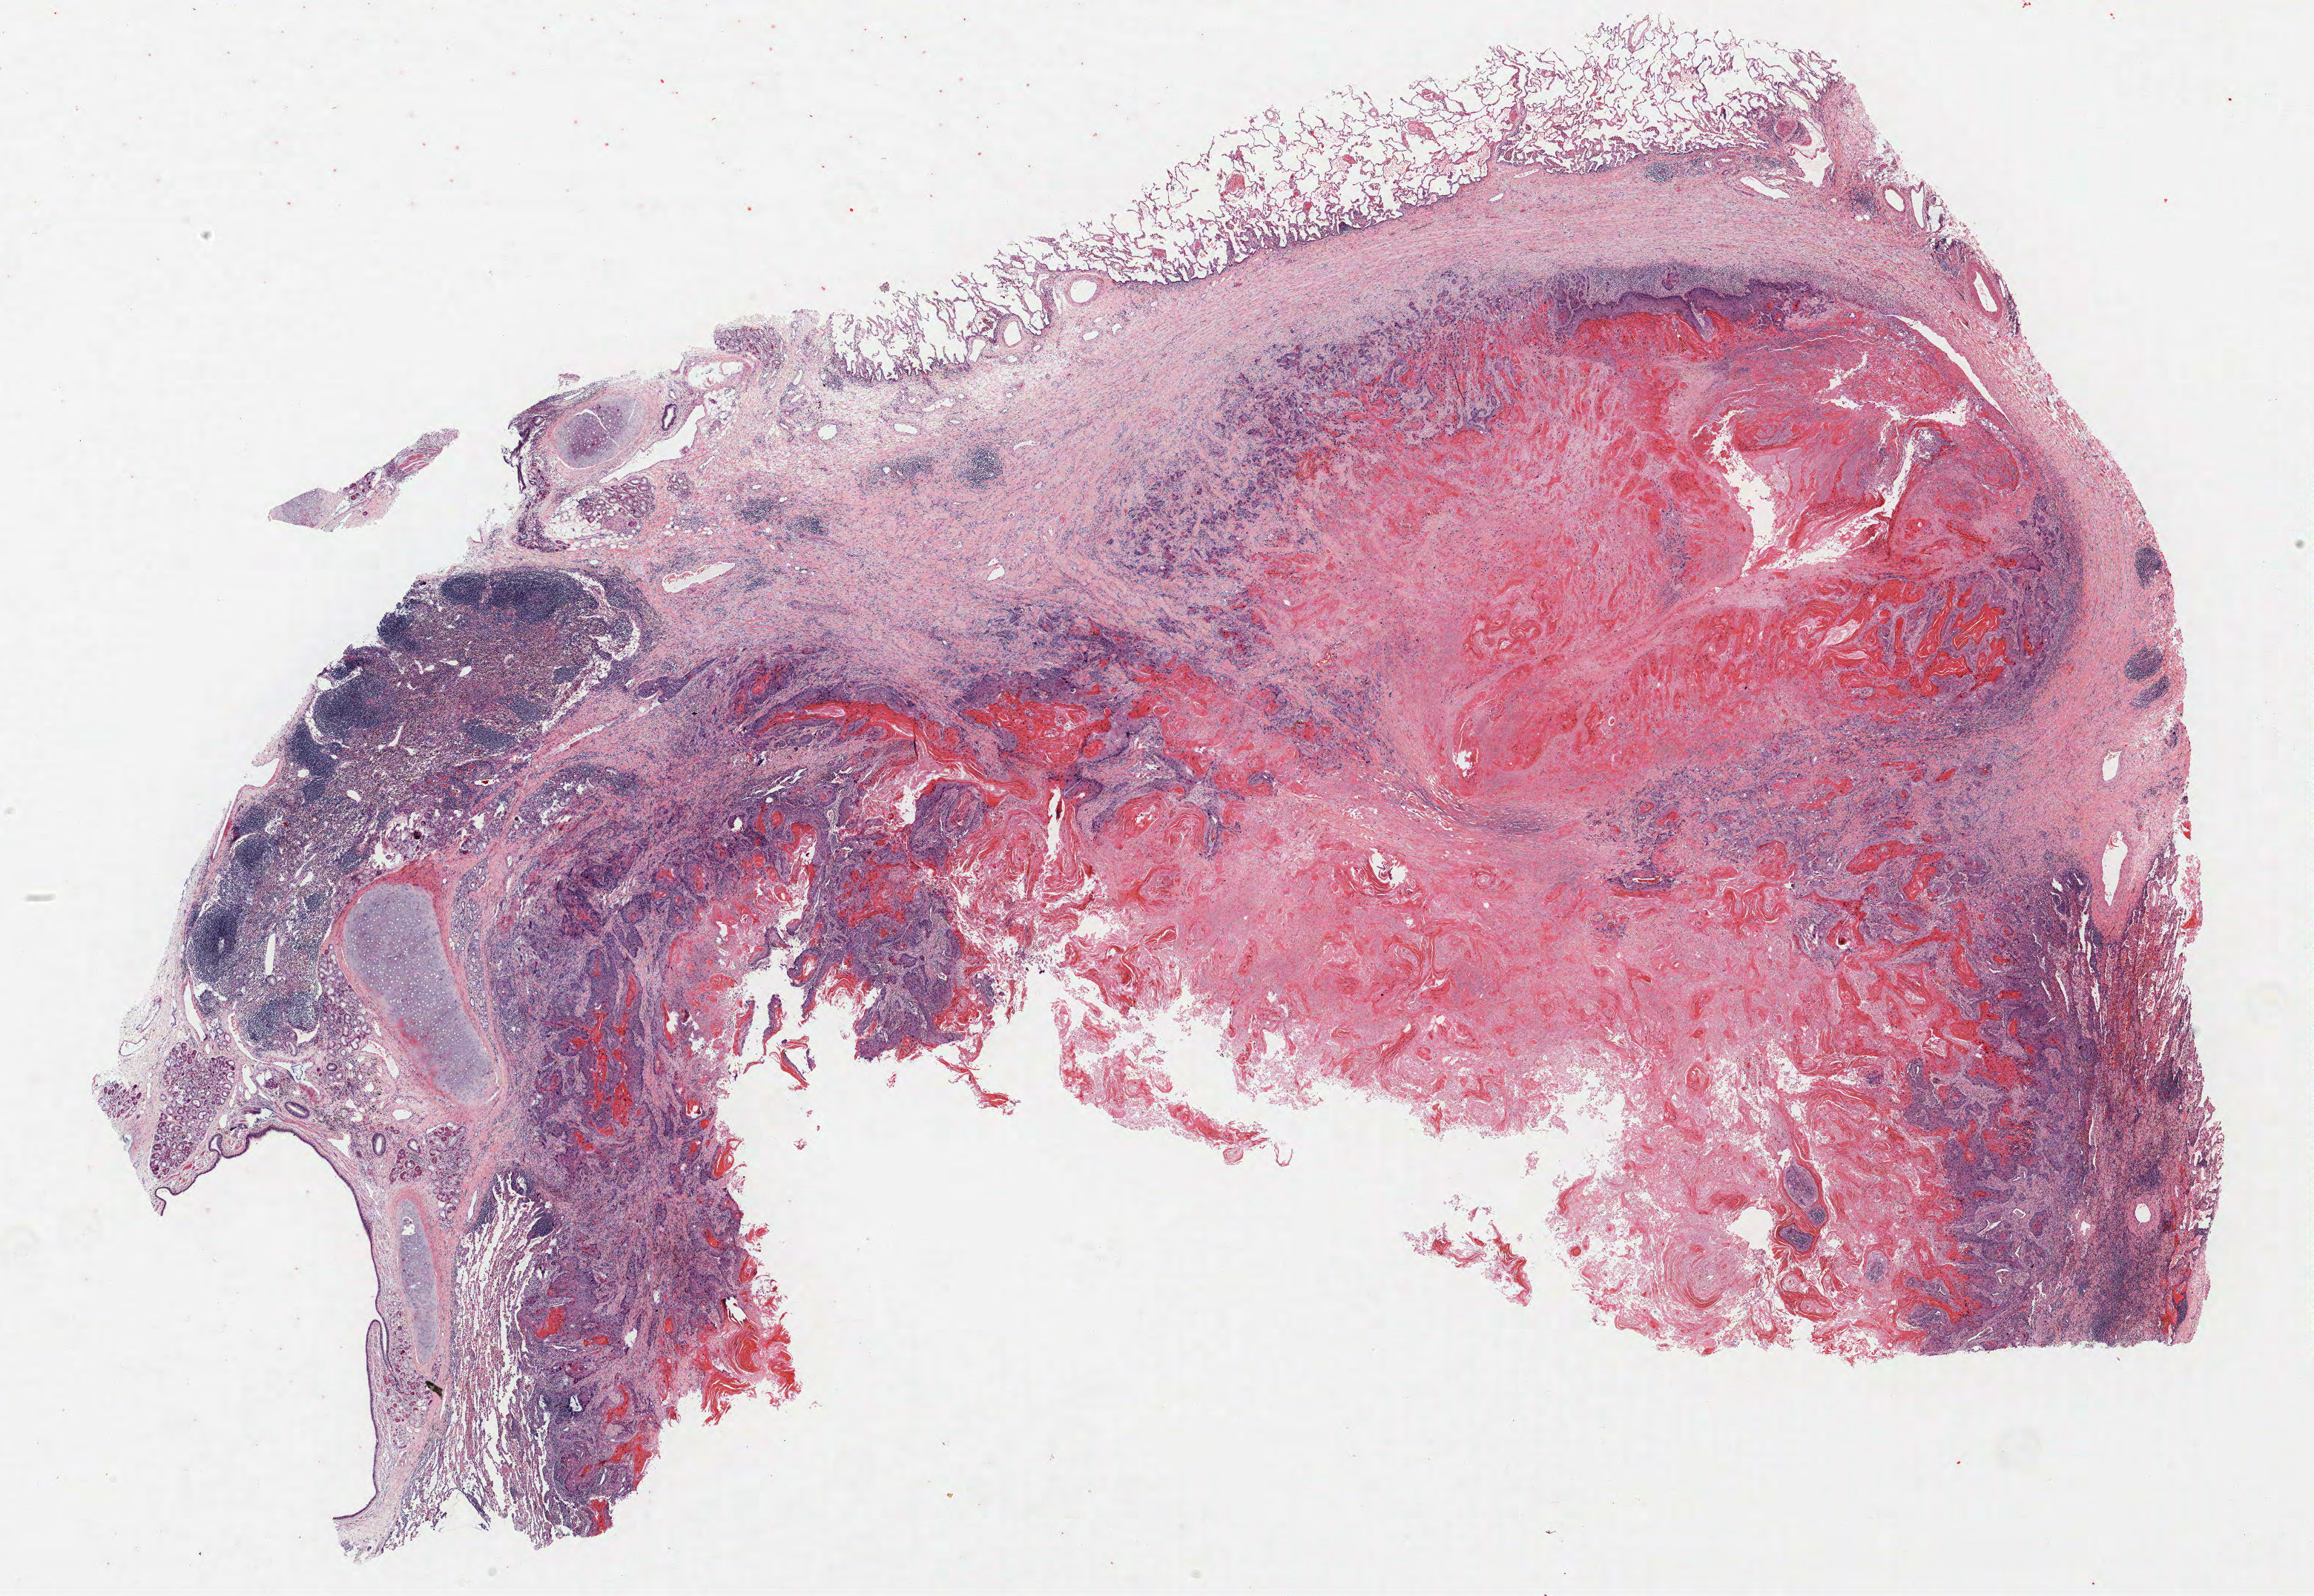
H&E whole-slide image — a low-resolution overview of the entire scanned area, about 25.0 x 17.2 mm, formalin-fixed paraffin-embedded (FFPE) section, lung. Male patient, aged 57 at enrolment. Current smoker at enrolment. Grade: moderately differentiated (G2).
* stage (AJCC 6th edition): IB
* ICD-O-3 topography: lower lobe of lung (C34.3)
* tumour size (pathology): 35 mm
* primary tumour location (clinical record): left lower lobe
* participant's lung-cancer diagnosis: Squamous cell carcinoma, NOS (ICD-O-3 8070/3)